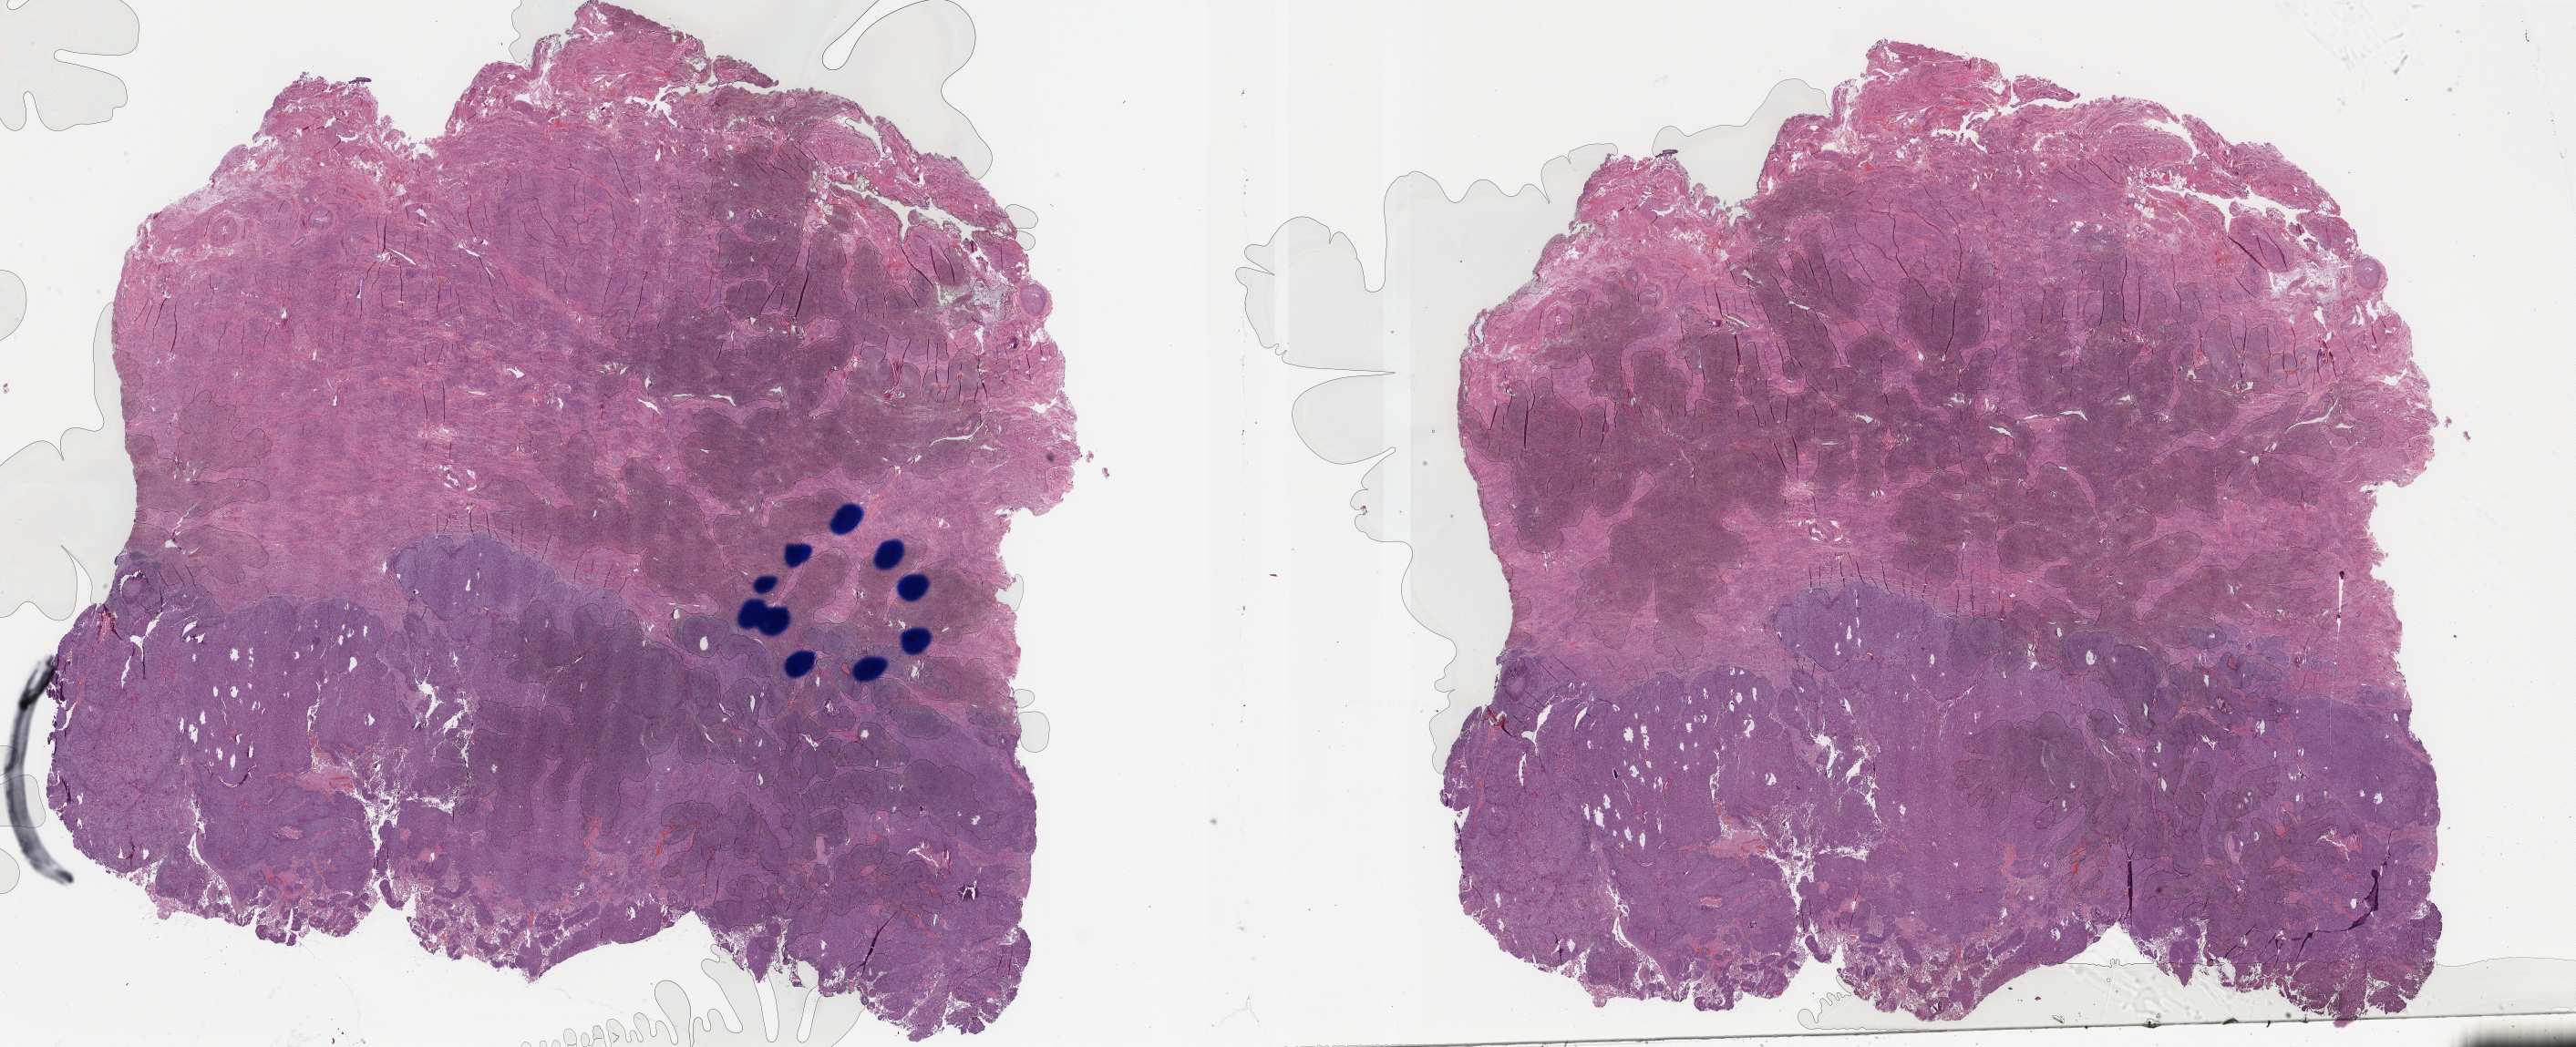
H&E-stained whole-slide image, a low-resolution overview of the entire scanned area, about 44.9 x 18.2 mm; FFPE section; uterus, primary tumour sample. Female patient; age at initial diagnosis 69 years. Histologic grade: G3 (poorly differentiated).
FIGO stage: IVB. Diagnosis: Endometrioid adenocarcinoma, NOS.